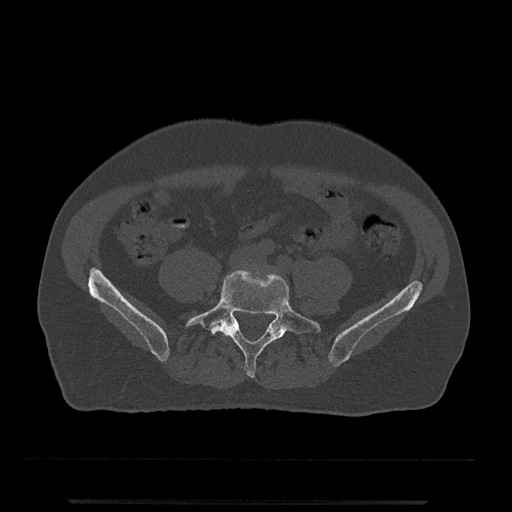
CT including the spine, one axial slice. Position 78 of 797 along the scan axis. Reconstruction kernel Br40s/3. 120 kVp. Bone window (W 1800 / L 400 HU). 512 × 512 image matrix, field of view 419 × 419 mm. Male patient, age 63 years. Case-level facts recorded for this patient, not image findings: primary cancer: prostate.
Structures marked on this image (semi-automatically segmented with operator editing):
- L4 vertebra: bounding box (x1, y1, x2, y2) in pixels: (232, 320, 234, 323)
- L5 vertebra: (185, 270, 321, 378)